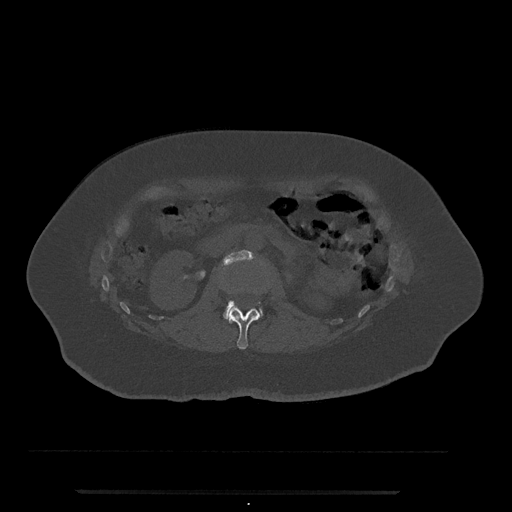
CT including the spine, one axial slice. Position 74 of 797 along the scan axis. 120 kVp. Bone window (W 1800 / L 400 HU). 0.5 mm slice thickness. 512 × 512 image matrix. Patient: female, 51 years. From the clinical record (not read from this slice): primary cancer: neuro; vertebrae with lytic lesions (as recorded): T8.
Structures marked on this image (semi-automatically segmented with operator editing):
- L1 vertebra: bounding box [x1, y1, x2, y2] px = [224, 307, 261, 350]
- L2 vertebra: [224, 250, 263, 318]